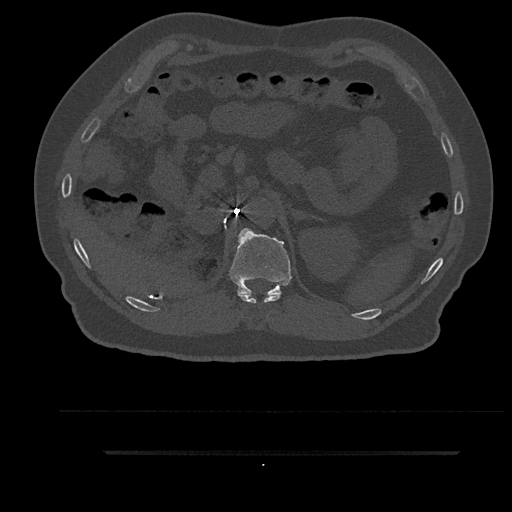
CT including the spine, one axial slice. Position 266 of 797 along the scan axis. Reconstruction kernel Br40s/3. 120 kVp. Bone window (W 1800 / L 400 HU). 0.5 mm slice thickness. 512 × 512 image matrix, field of view 432 × 432 mm. Patient: male, 63 years. From the clinical record (not read from this slice): primary cancer: renal; vertebrae with lytic lesions (as recorded): T8.
Structures marked on this image (semi-automatically segmented with operator editing):
- T11 vertebra: bounding box [x1, y1, x2, y2] px = [238, 293, 281, 304]
- T12 vertebra: [229, 228, 292, 296]